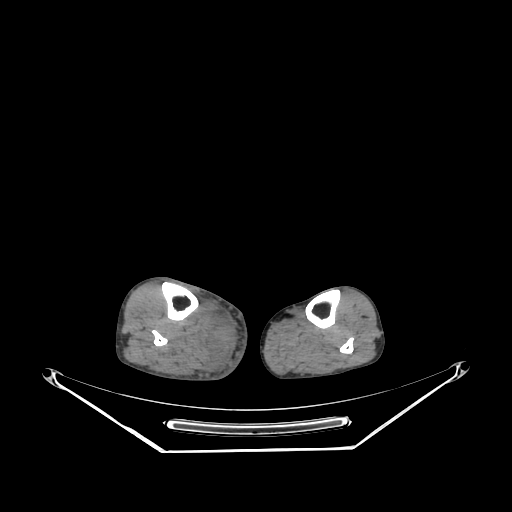
CT of an extremity soft-tissue mass (from a PET/CT study), one axial slice. Slice 125 of 267 in the series (ordered by position). 140 kVp. Soft-tissue window (W 400 / L 40 HU). 3.75 mm slice thickness. 512 × 512 image matrix, field of view 500 × 500 mm. Male patient. From the clinical record (not read from this slice): histological type: pleiomorphic liposarcoma; grade: high; site of the primary tumour: right calf.
Structures marked on this image (expert contour drawn on MRI and transferred to this co-registered scan by the dataset authors):
- gross tumour volume including surrounding oedema: bounding box <206,313,236,368> (left, top, right, bottom; pixels)
- gross tumour volume (mass): <212,322,229,341>